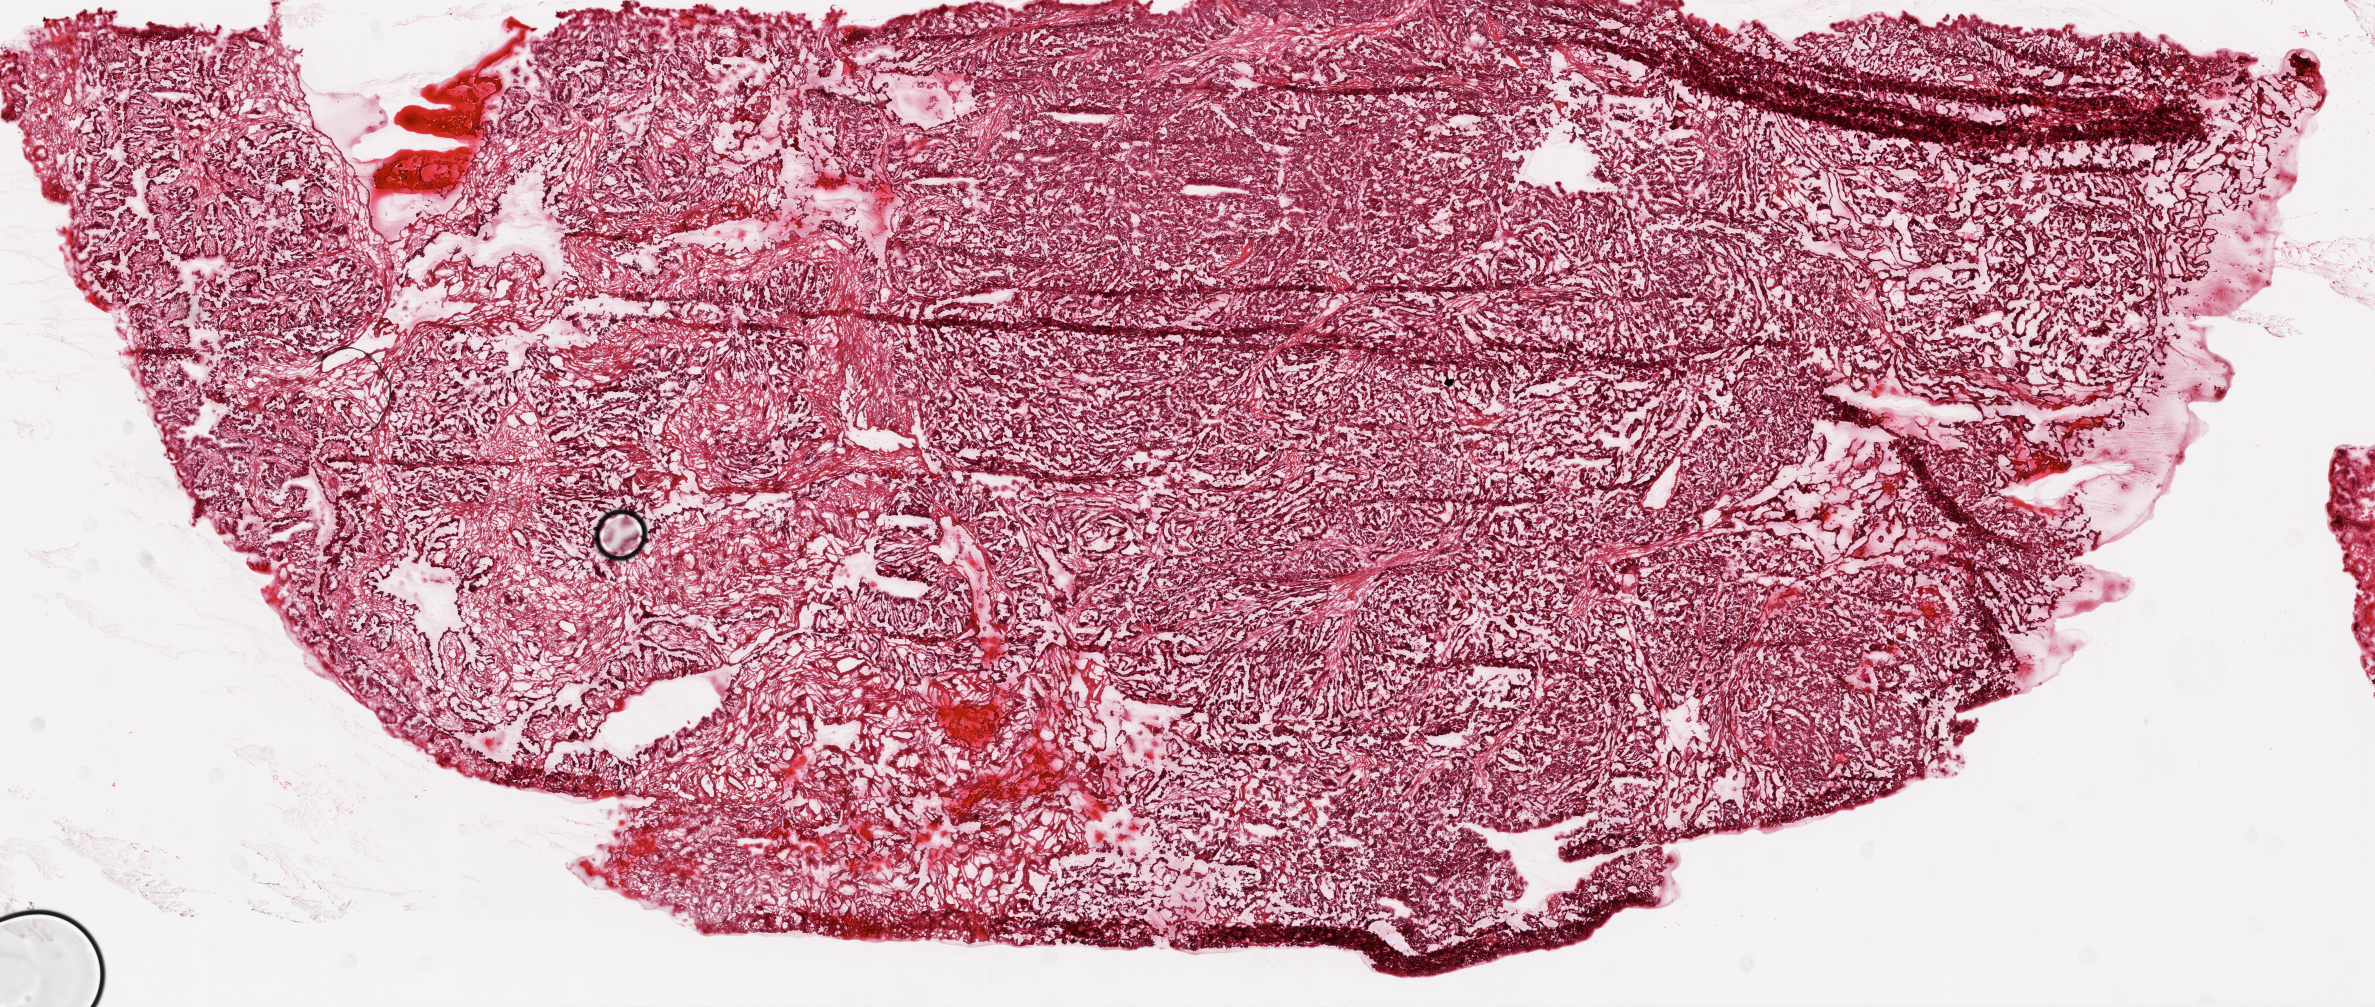
H&E-stained whole-slide image — low-resolution overview of the scanned area, about 19.1 x 8.1 mm (acquisition: 20x scan). Frozen section. Sample: primary tumour, ovary. Female patient; age at initial diagnosis 50 years. Histologic grade: G3 (poorly differentiated). Pathologist review of this section (percent, as recorded): tumour cells 90%, tumour nuclei 85%, normal cells 0%, stromal cells 10%, necrosis 0%.
FIGO stage: IIB. Histologic diagnosis: Serous cystadenocarcinoma, NOS.